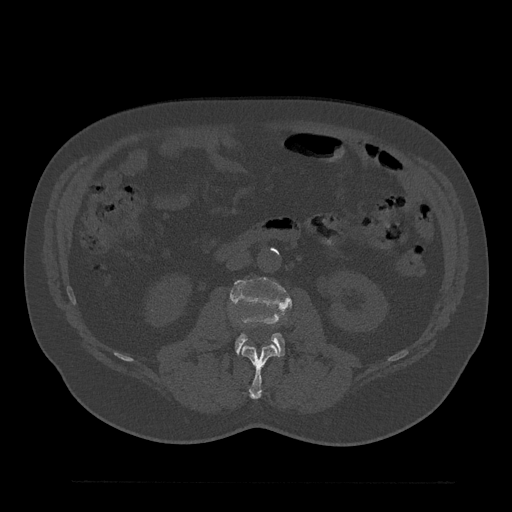
CT including the spine, one axial slice. Position 67 of 797 along the scan axis. Bone window (W 1800 / L 400 HU). 0.5 mm slice thickness. 512 × 512 image matrix, field of view 430 × 430 mm. Patient: male, 61 years. Case-level facts recorded for this patient, not image findings: primary cancer: prostate.
Annotated regions visible in this slice (semi-automatic segmentation, software-assisted and operator-edited):
- L2 vertebra: bounding box [x1, y1, x2, y2] px = [241, 344, 279, 399]
- L3 vertebra: [231, 277, 292, 356]